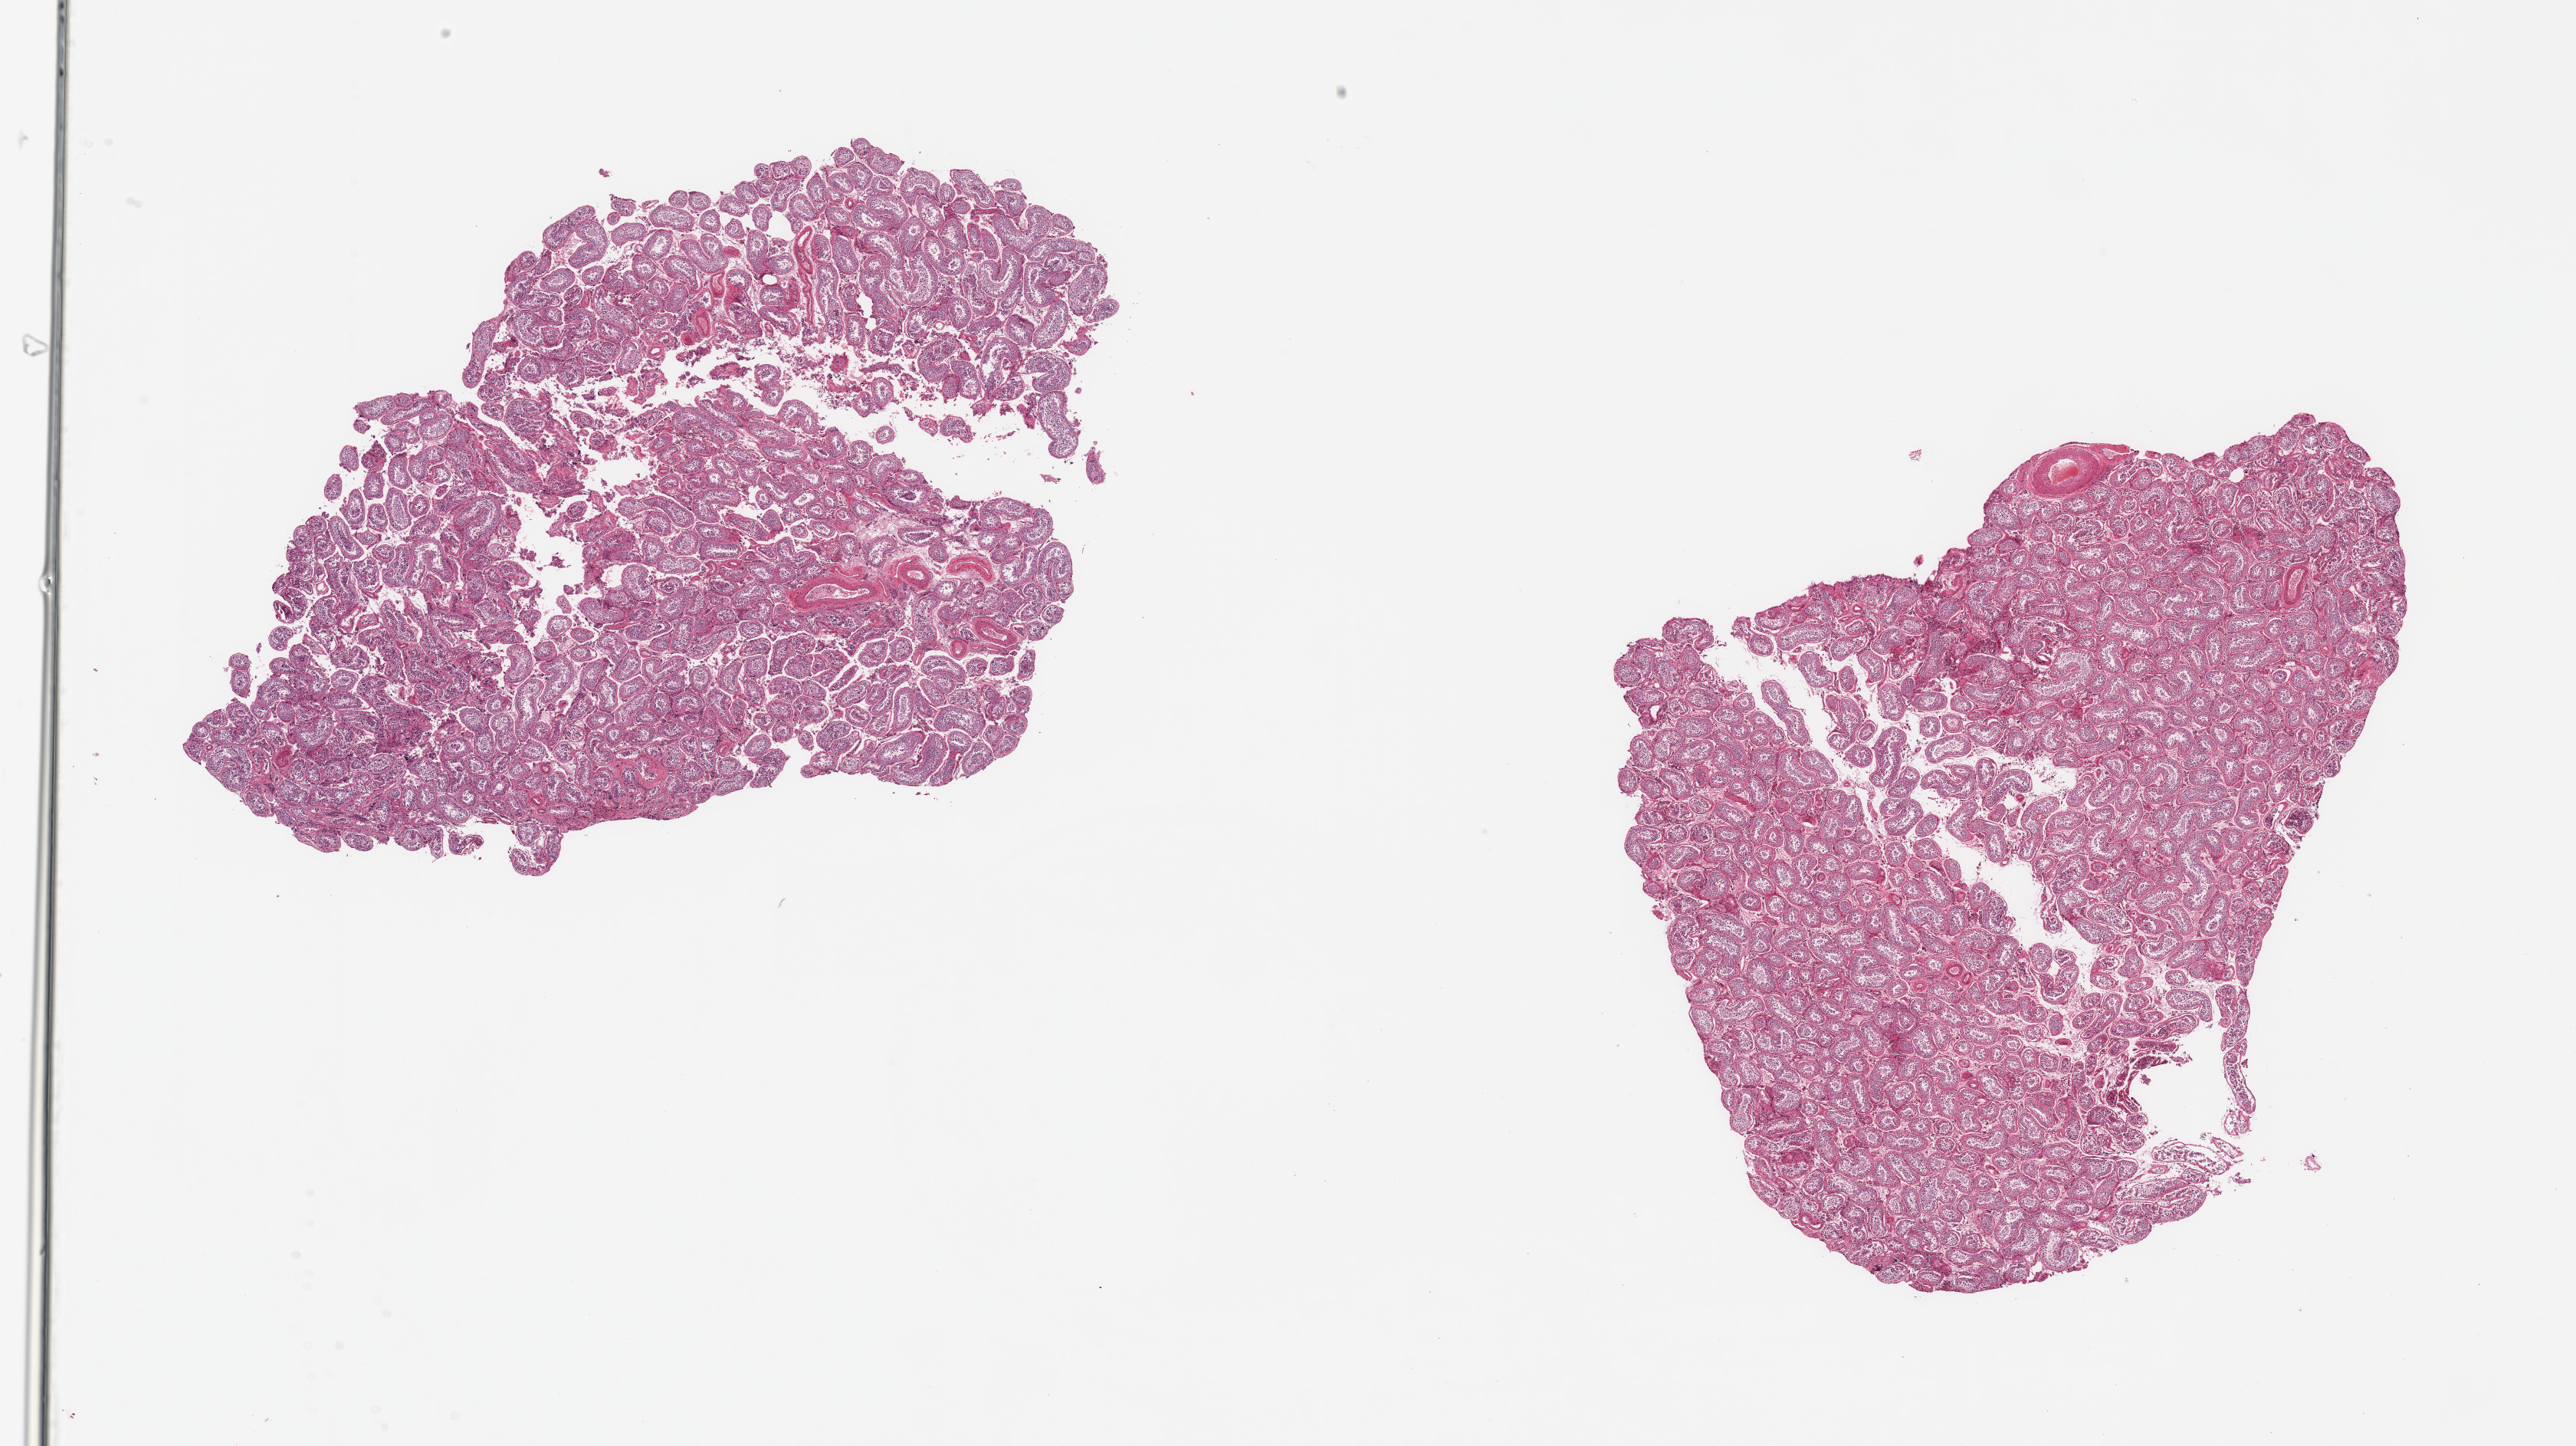
Haematoxylin and eosin whole-slide image, shown as a low-resolution overview of the whole scanned area (about 26.6 x 14.9 mm, from a 20x scan); PAXgene-fixed, paraffin-embedded tissue; target tissue: testis; donor tissue sample. Donor: male.
Review note (as recorded): 2 pieces, reduced spermatogenesis.